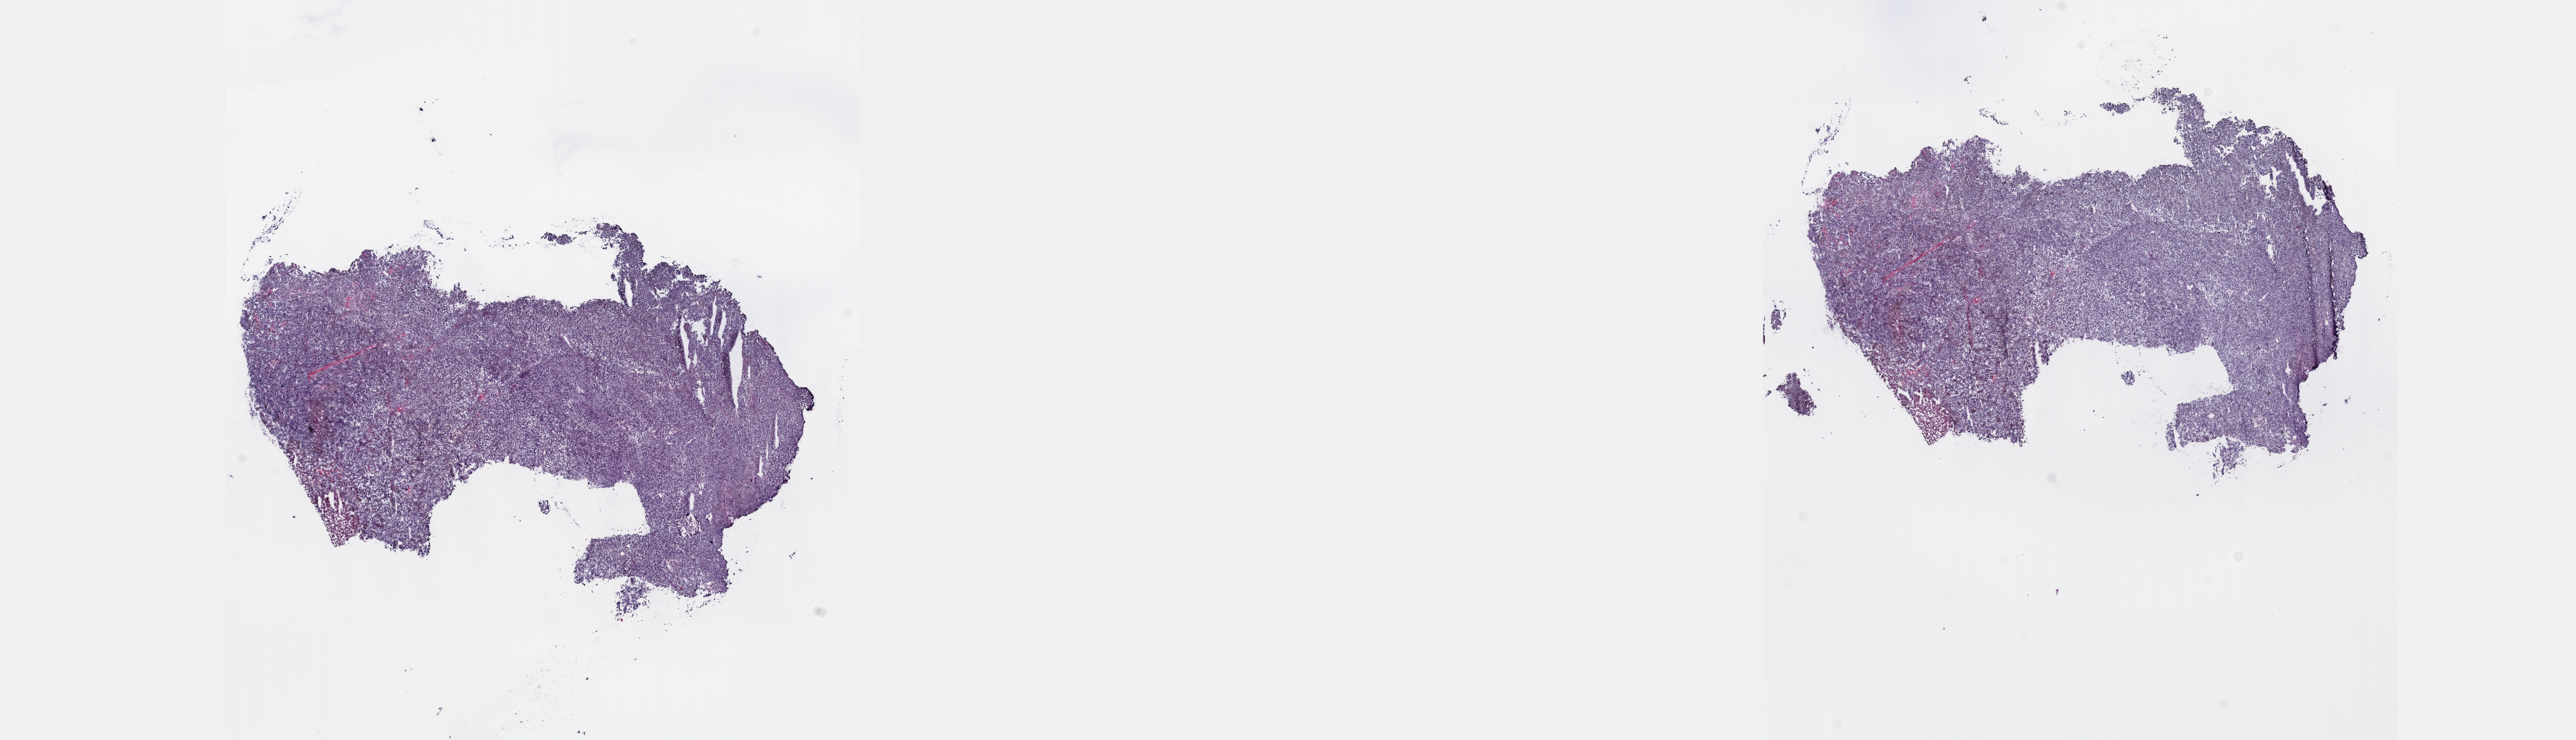
H&E whole-slide image, whole scanned area (about 28.7 x 8.2 mm) shown as a low-resolution overview, frozen section from the top of the tissue portion, metastatic tumour sample. Male patient; age at initial diagnosis 57 years. Composition of this section per pathologist review: tumour cells 85%, tumour nuclei 85%, normal cells 0%, stromal cells 11%, necrosis 4%. Inflammatory infiltration, as recorded: lymphocyte infiltration 2%, monocyte infiltration 1%, neutrophil infiltration 1%.
* this section: metastatic tumour tissue
* patient diagnosis: Malignant melanoma, NOS